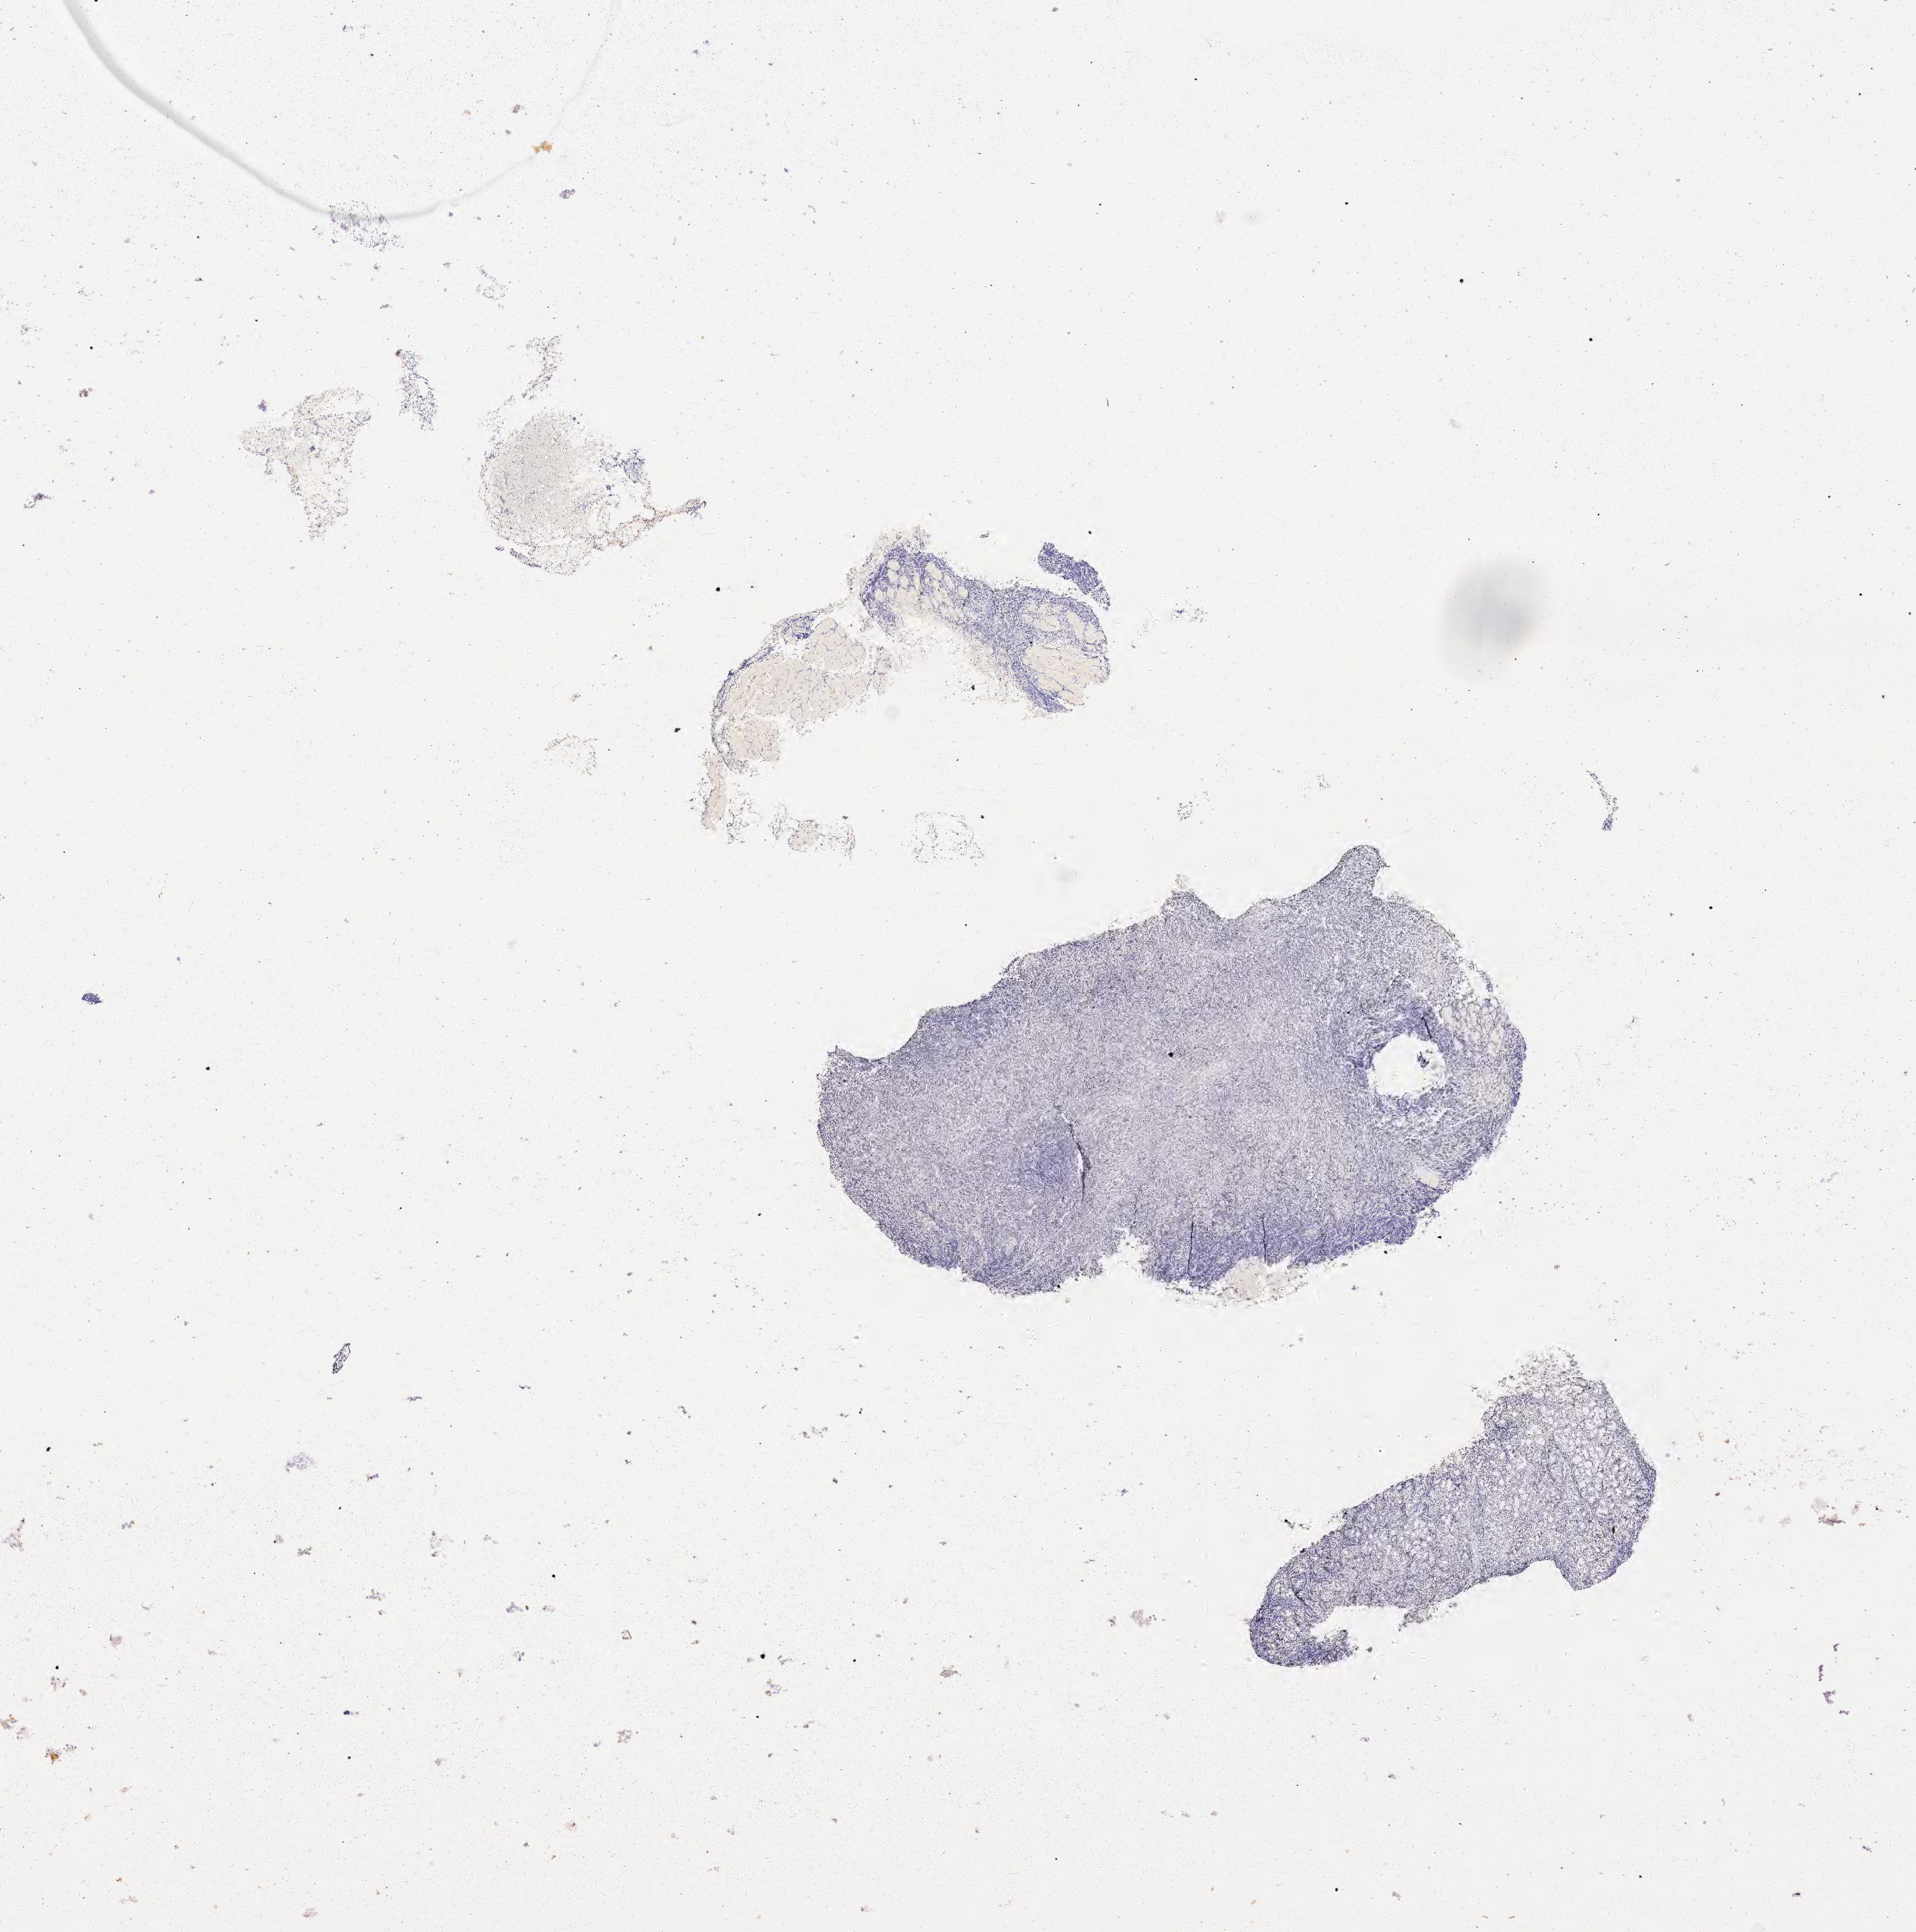
In-situ hybridisation whole-slide image, Epstein–Barr virus-encoded RNA (EBER) probe, shown as a low-resolution overview of the whole scanned area (about 11.1 x 11.2 mm); tumor tissue. Patient male; aged 53.
Diagnosis: Diffuse large B-cell lymphoma, NOS.